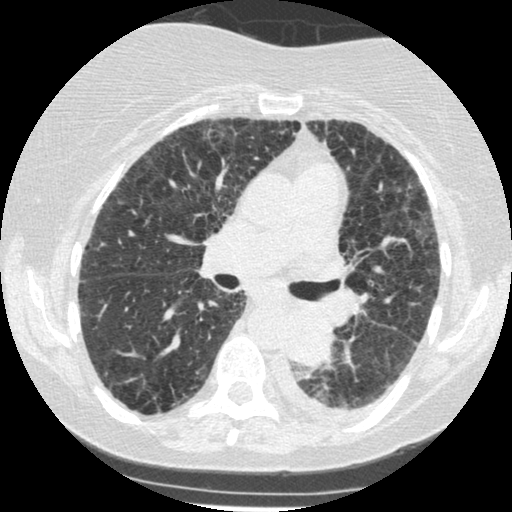
Axial slice from a low-dose chest CT screening exam; third annual screen; lung window (W 1500 / L -600 HU); 1.25 mm slice thickness; 512 × 512 image matrix. Female, age 60 years at enrolment. Former smoker at enrolment.
Lesion marked by an expert reader, box from (x=270, y=307) to (x=342, y=373) px. Reader record for this screening exam (exam-level; its link to the box is not recorded): non-calcified nodule or mass ≥4 mm, left lower lobe, 54 × 38 mm, smooth margins, soft tissue attenuation, pre-existing on the prior screen: yes; interval growth: yes. Lung cancer was diagnosed 15 days after this screen: small cell carcinoma, NOS, left lower lobe, undifferentiated (G4), stage IV (AJCC 6th edition), 69 mm at pathology.